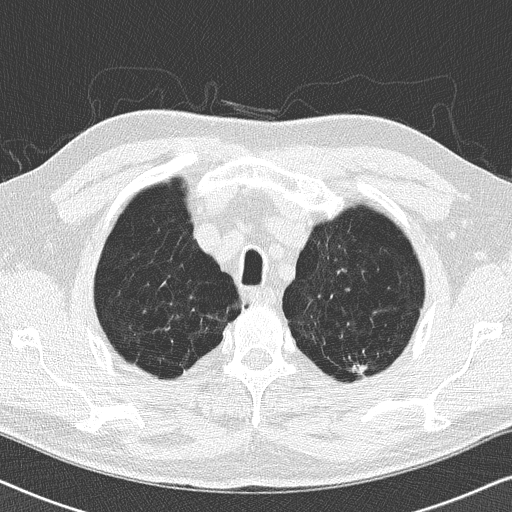
Axial slice from a low-dose chest CT screening exam, second annual screen, lung window (W 1500 / L -600 HU), lung (sharp) reconstruction kernel (B50f), slice 23 of 175 in the series, 512 × 512 image matrix. Male, age 62 years at enrolment.
• Expert-annotated lung lesion, bounding box [x1, y1, x2, y2] px = [340, 351, 380, 386].
• The exam's reader record, not a measurement of the box and not confirmed to be the same lesion: non-calcified nodule or mass ≥4 mm, left upper lobe, 10 × 10 mm, soft tissue attenuation, pre-existing on the prior screen: yes; interval growth: no.
• Participant outcome: lung cancer diagnosed 219 days after this screen — adenocarcinoma, NOS, left upper lobe, moderately differentiated (G2), stage IA (AJCC 6th edition), 10 mm at pathology.